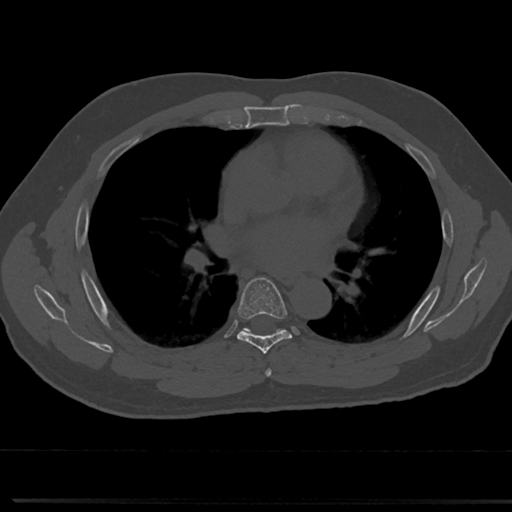
CT including the spine, one axial slice; slice 448 of 817 in the series (ordered by position); reconstruction kernel Br40s/3; bone window (W 1800 / L 400 HU); 0.5 mm slice thickness; 512 × 512 image matrix, field of view 355 × 355 mm. Patient: male, 61 years. Case-level facts recorded for this patient, not image findings: primary cancer: prostate.
Annotated regions visible in this slice (semi-automatic segmentation, software-assisted and operator-edited):
- T5 vertebra: bounding box [x1, y1, x2, y2] px = [264, 350, 273, 376]
- T6 vertebra: [219, 277, 310, 354]